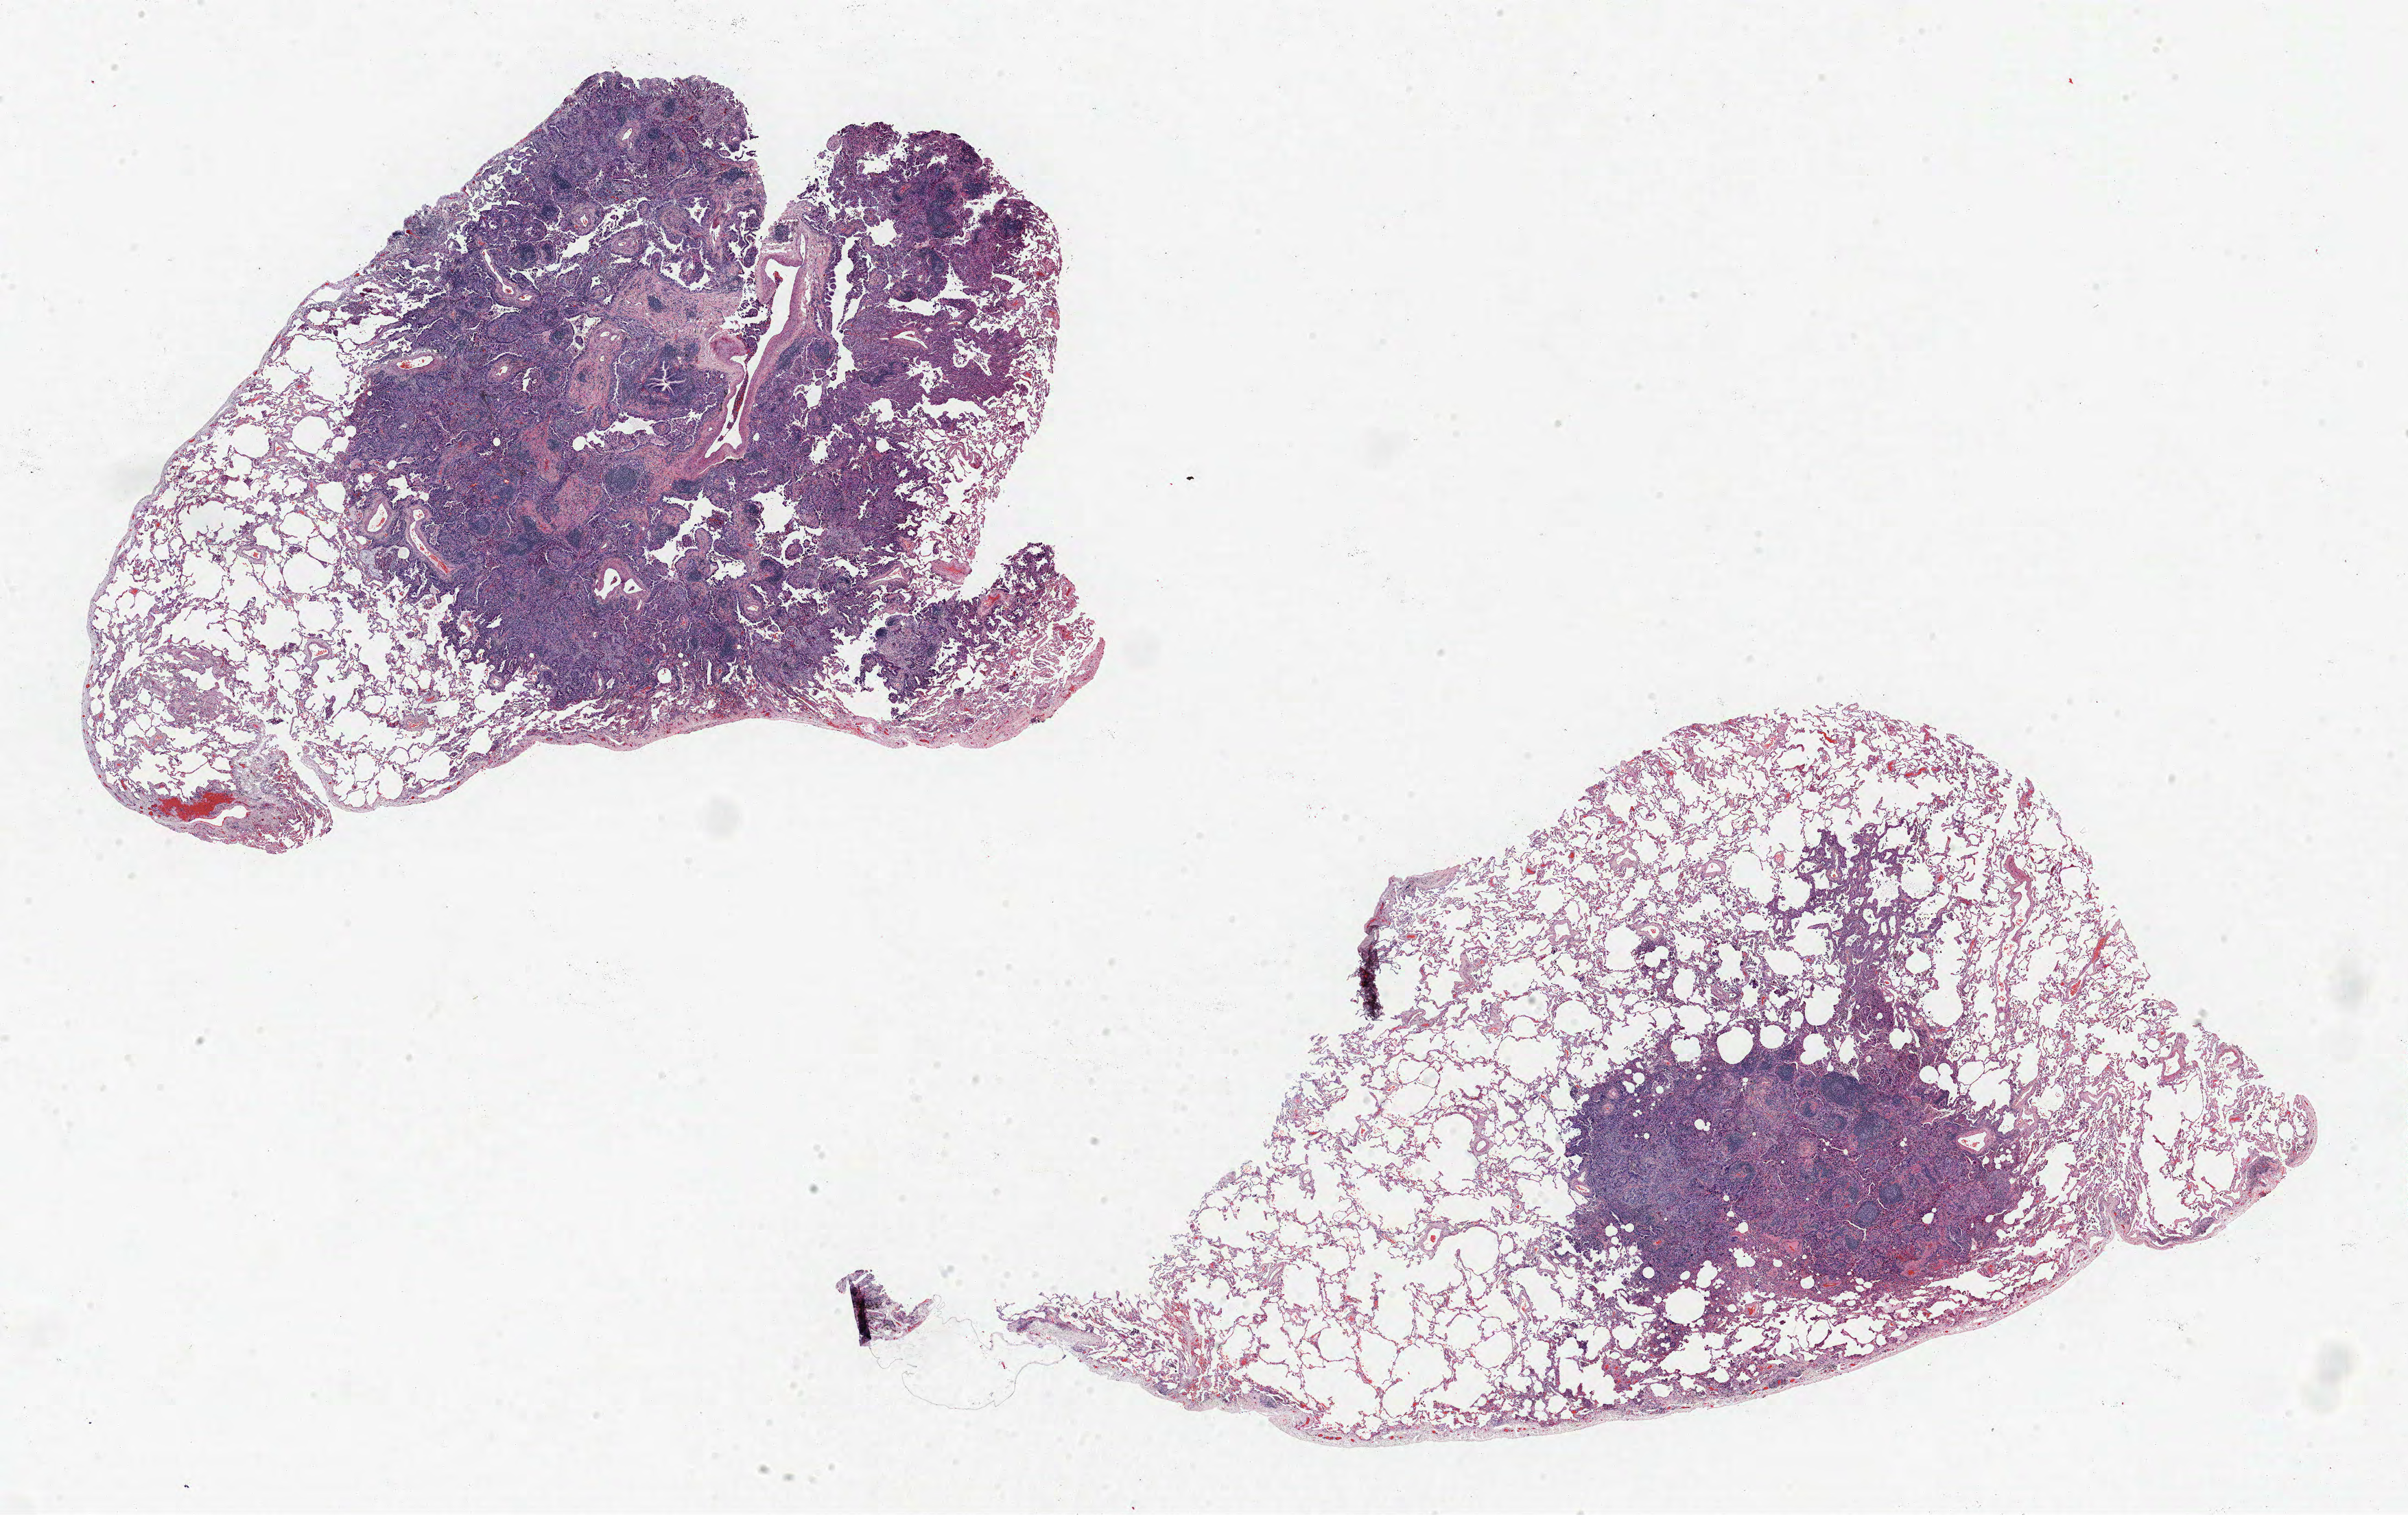
Whole-slide histology image, H&E — shown as a low-resolution overview of the whole scanned area (about 28.1 x 17.7 mm, slide scanned at 40x); formalin-fixed paraffin-embedded (FFPE) section; lung tissue. Male patient, aged 65 at enrolment. Current smoker at enrolment.
Participant's lung-cancer diagnosis: Adenocarcinoma, NOS.